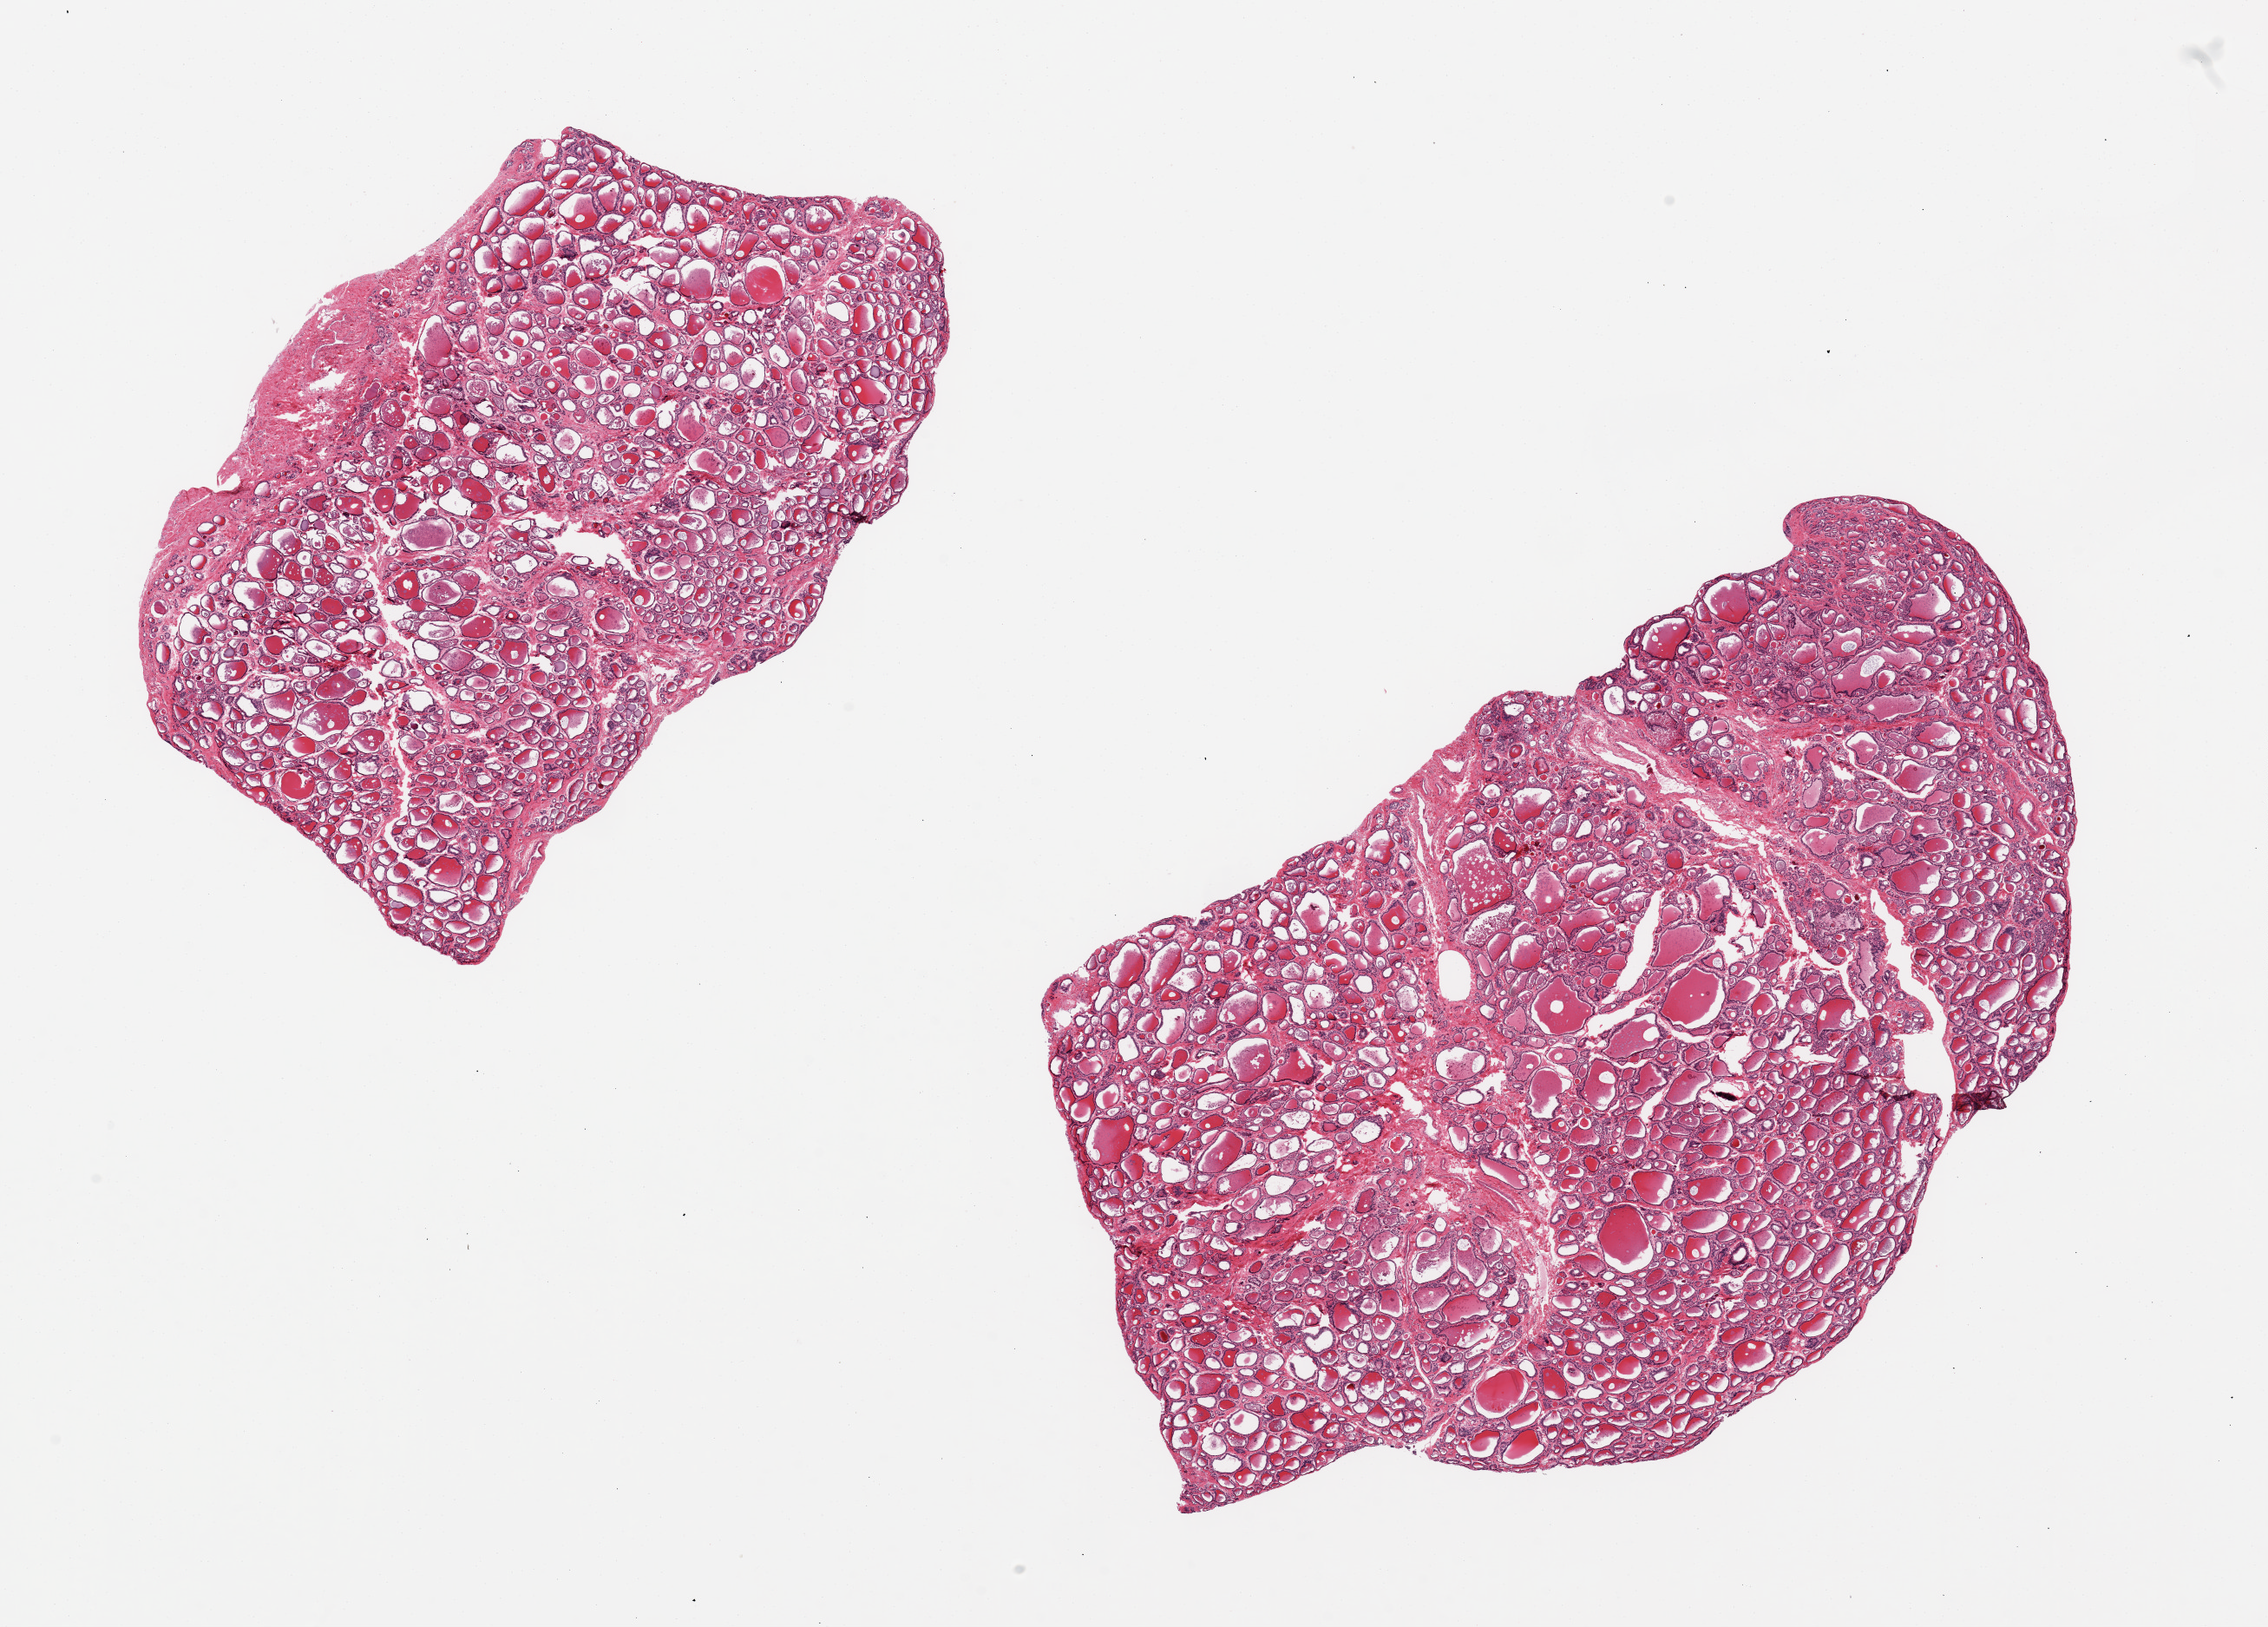
Whole-slide image, haematoxylin and eosin stain, whole scanned area (about 20.7 x 14.8 mm) shown as a low-resolution overview; PAXgene-fixed paraffin-embedded (PFPE) section; section of thyroid (target tissue); donor tissue sample.
Pathologist's review note for this sample: 2 pieces8x4 & 9x6 mm.